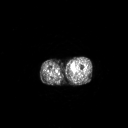
FDG PET of an extremity soft-tissue mass (from a PET/CT study), one axial slice; slice 230 of 267 in the series (ordered by position); 3.27 mm slice thickness; 128 × 128 image matrix, field of view 700 × 700 mm. Male patient, age 48 years. Case-level facts recorded for this patient, not image findings: histological type: pleiomorphic leiomyosarcoma; grade: high; site of the primary tumour: left thigh.
Outlined on this slice (expert contour drawn on MRI and transferred to this co-registered scan by the dataset authors):
- gross tumour volume including surrounding oedema: box from (x=69, y=64) to (x=75, y=70) px
- gross tumour volume (mass): (x=71, y=66)–(x=74, y=70)